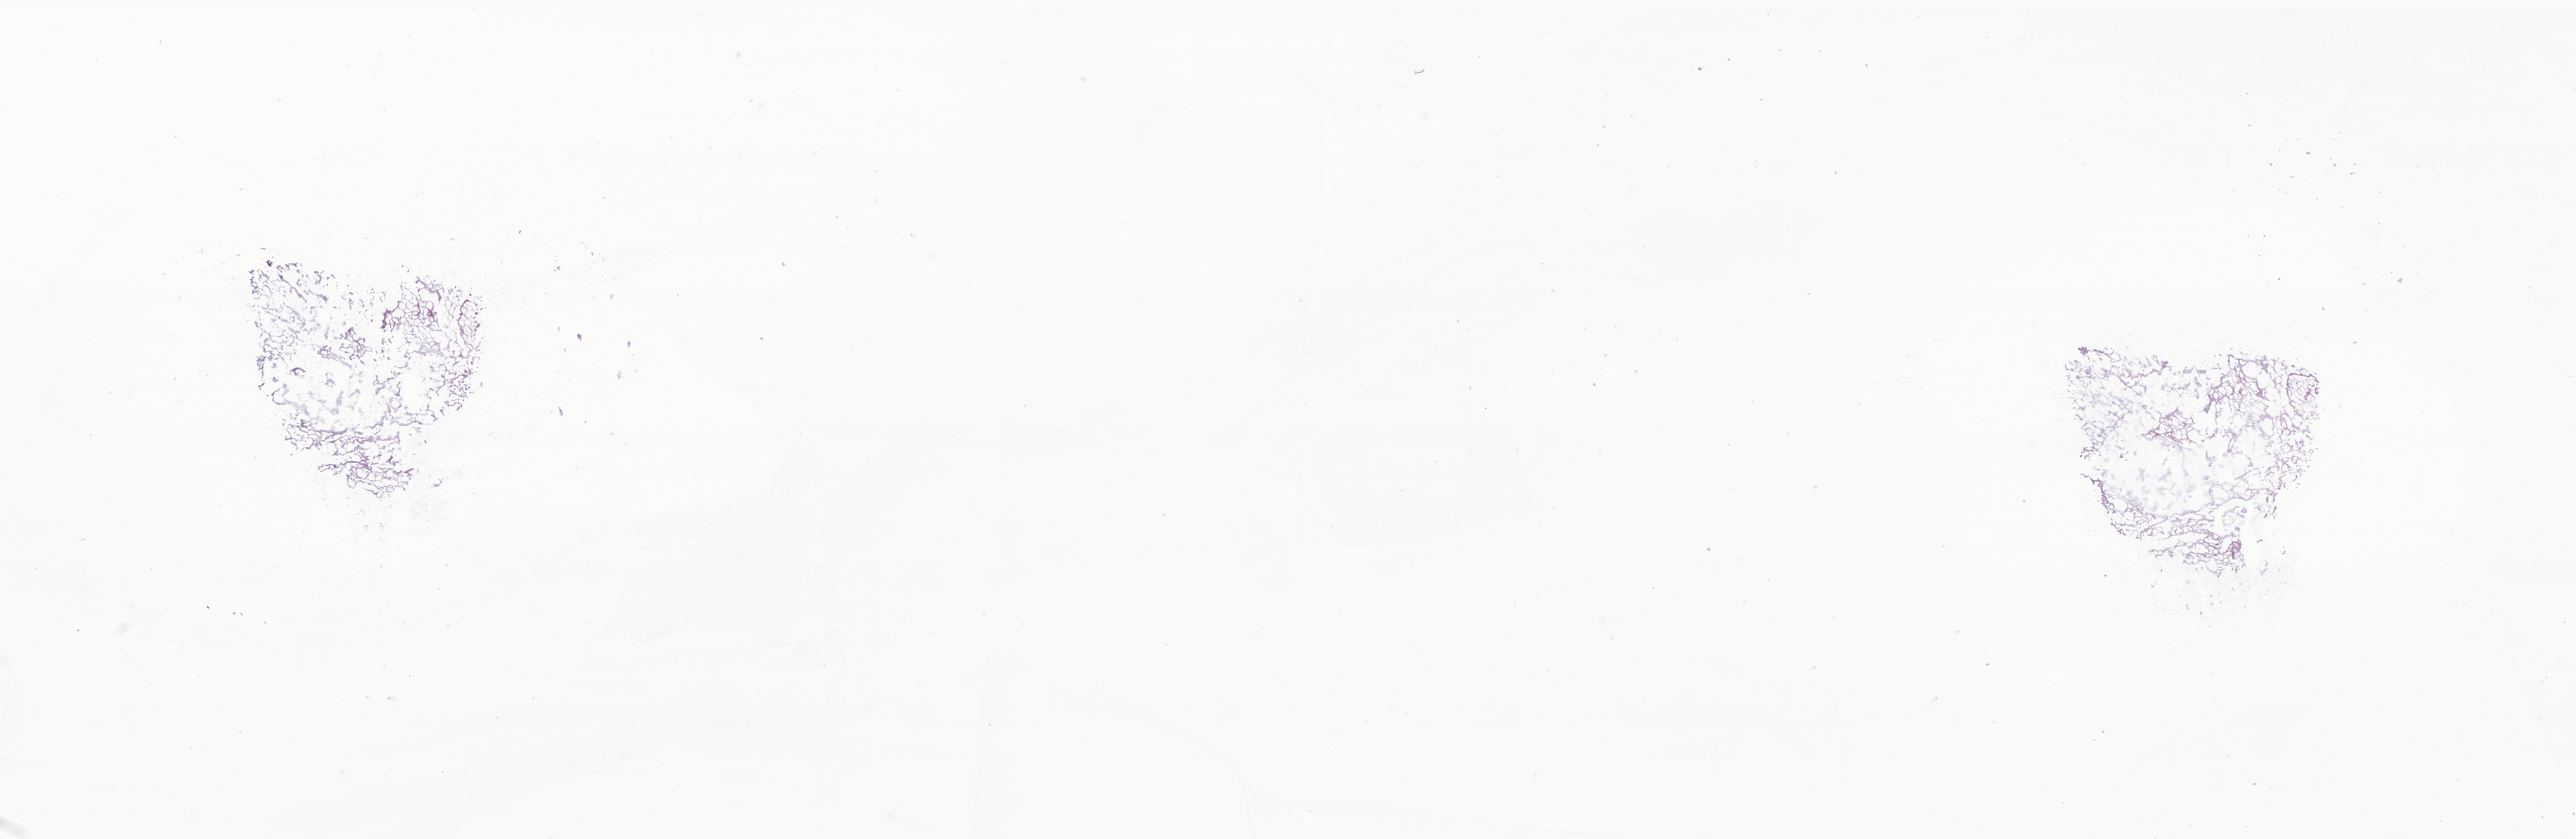
Whole-slide image, H&E stain of tumor tissue from the brain — shown as a low-resolution overview of the whole scanned area (about 19.8 x 6.4 mm). Cryosection (OCT / tissue freezing medium). Patient: female, age 99 months (8 years 3 months).
Diagnosis (ICD-O-3 morphology term): Ependymoma, NOS.